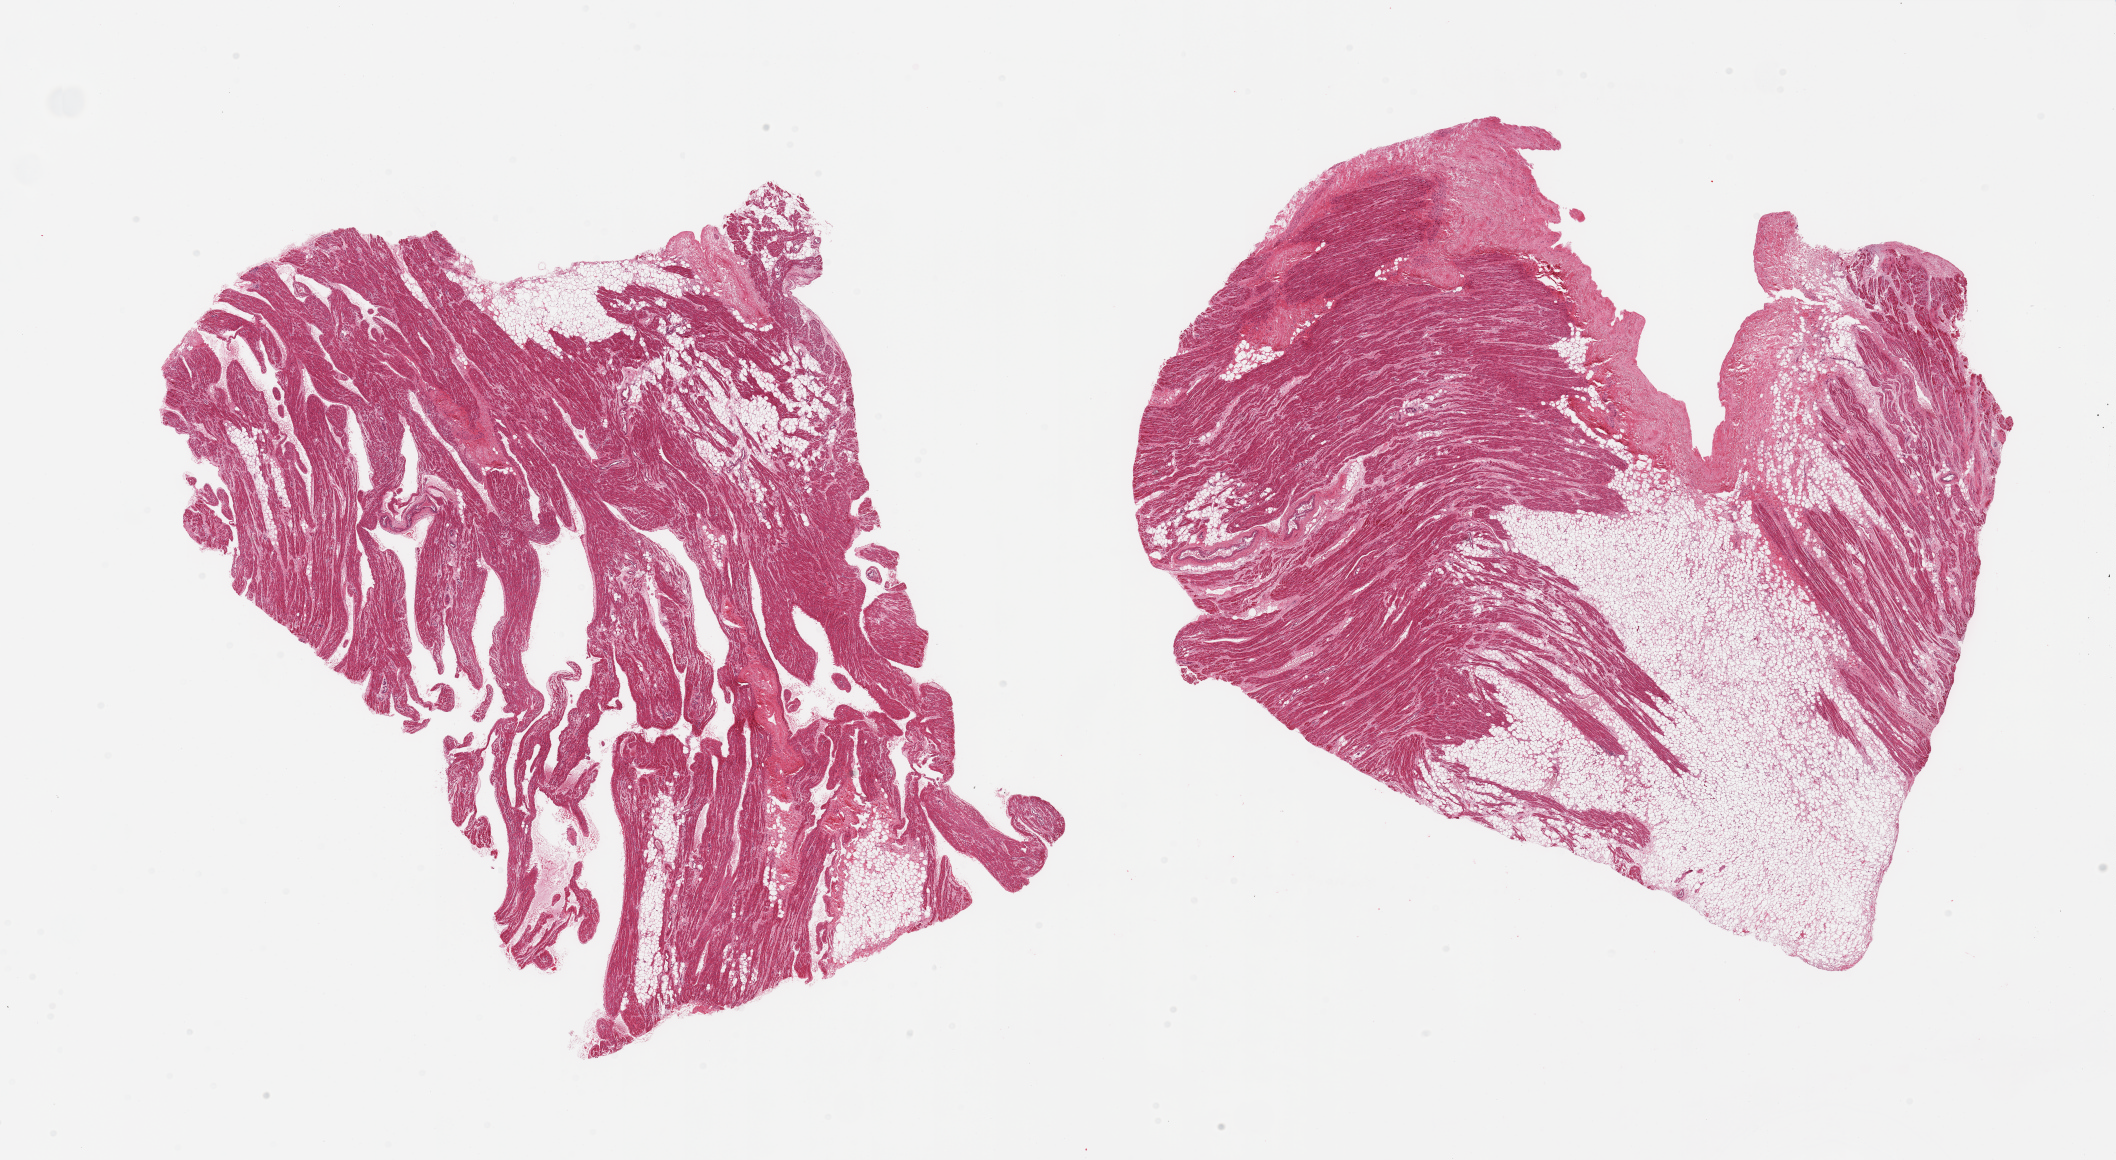
Digitized H&E-stained section — a low-resolution overview of the entire scanned area, about 33.5 x 18.3 mm; PAXgene-fixed, paraffin-embedded tissue; sampled site (target tissue): auricular appendage; tissue donor sample. Donor: female.
Reviewer comment on this tissue sample: 2 pieces, no abnormalities, ~25% fat.